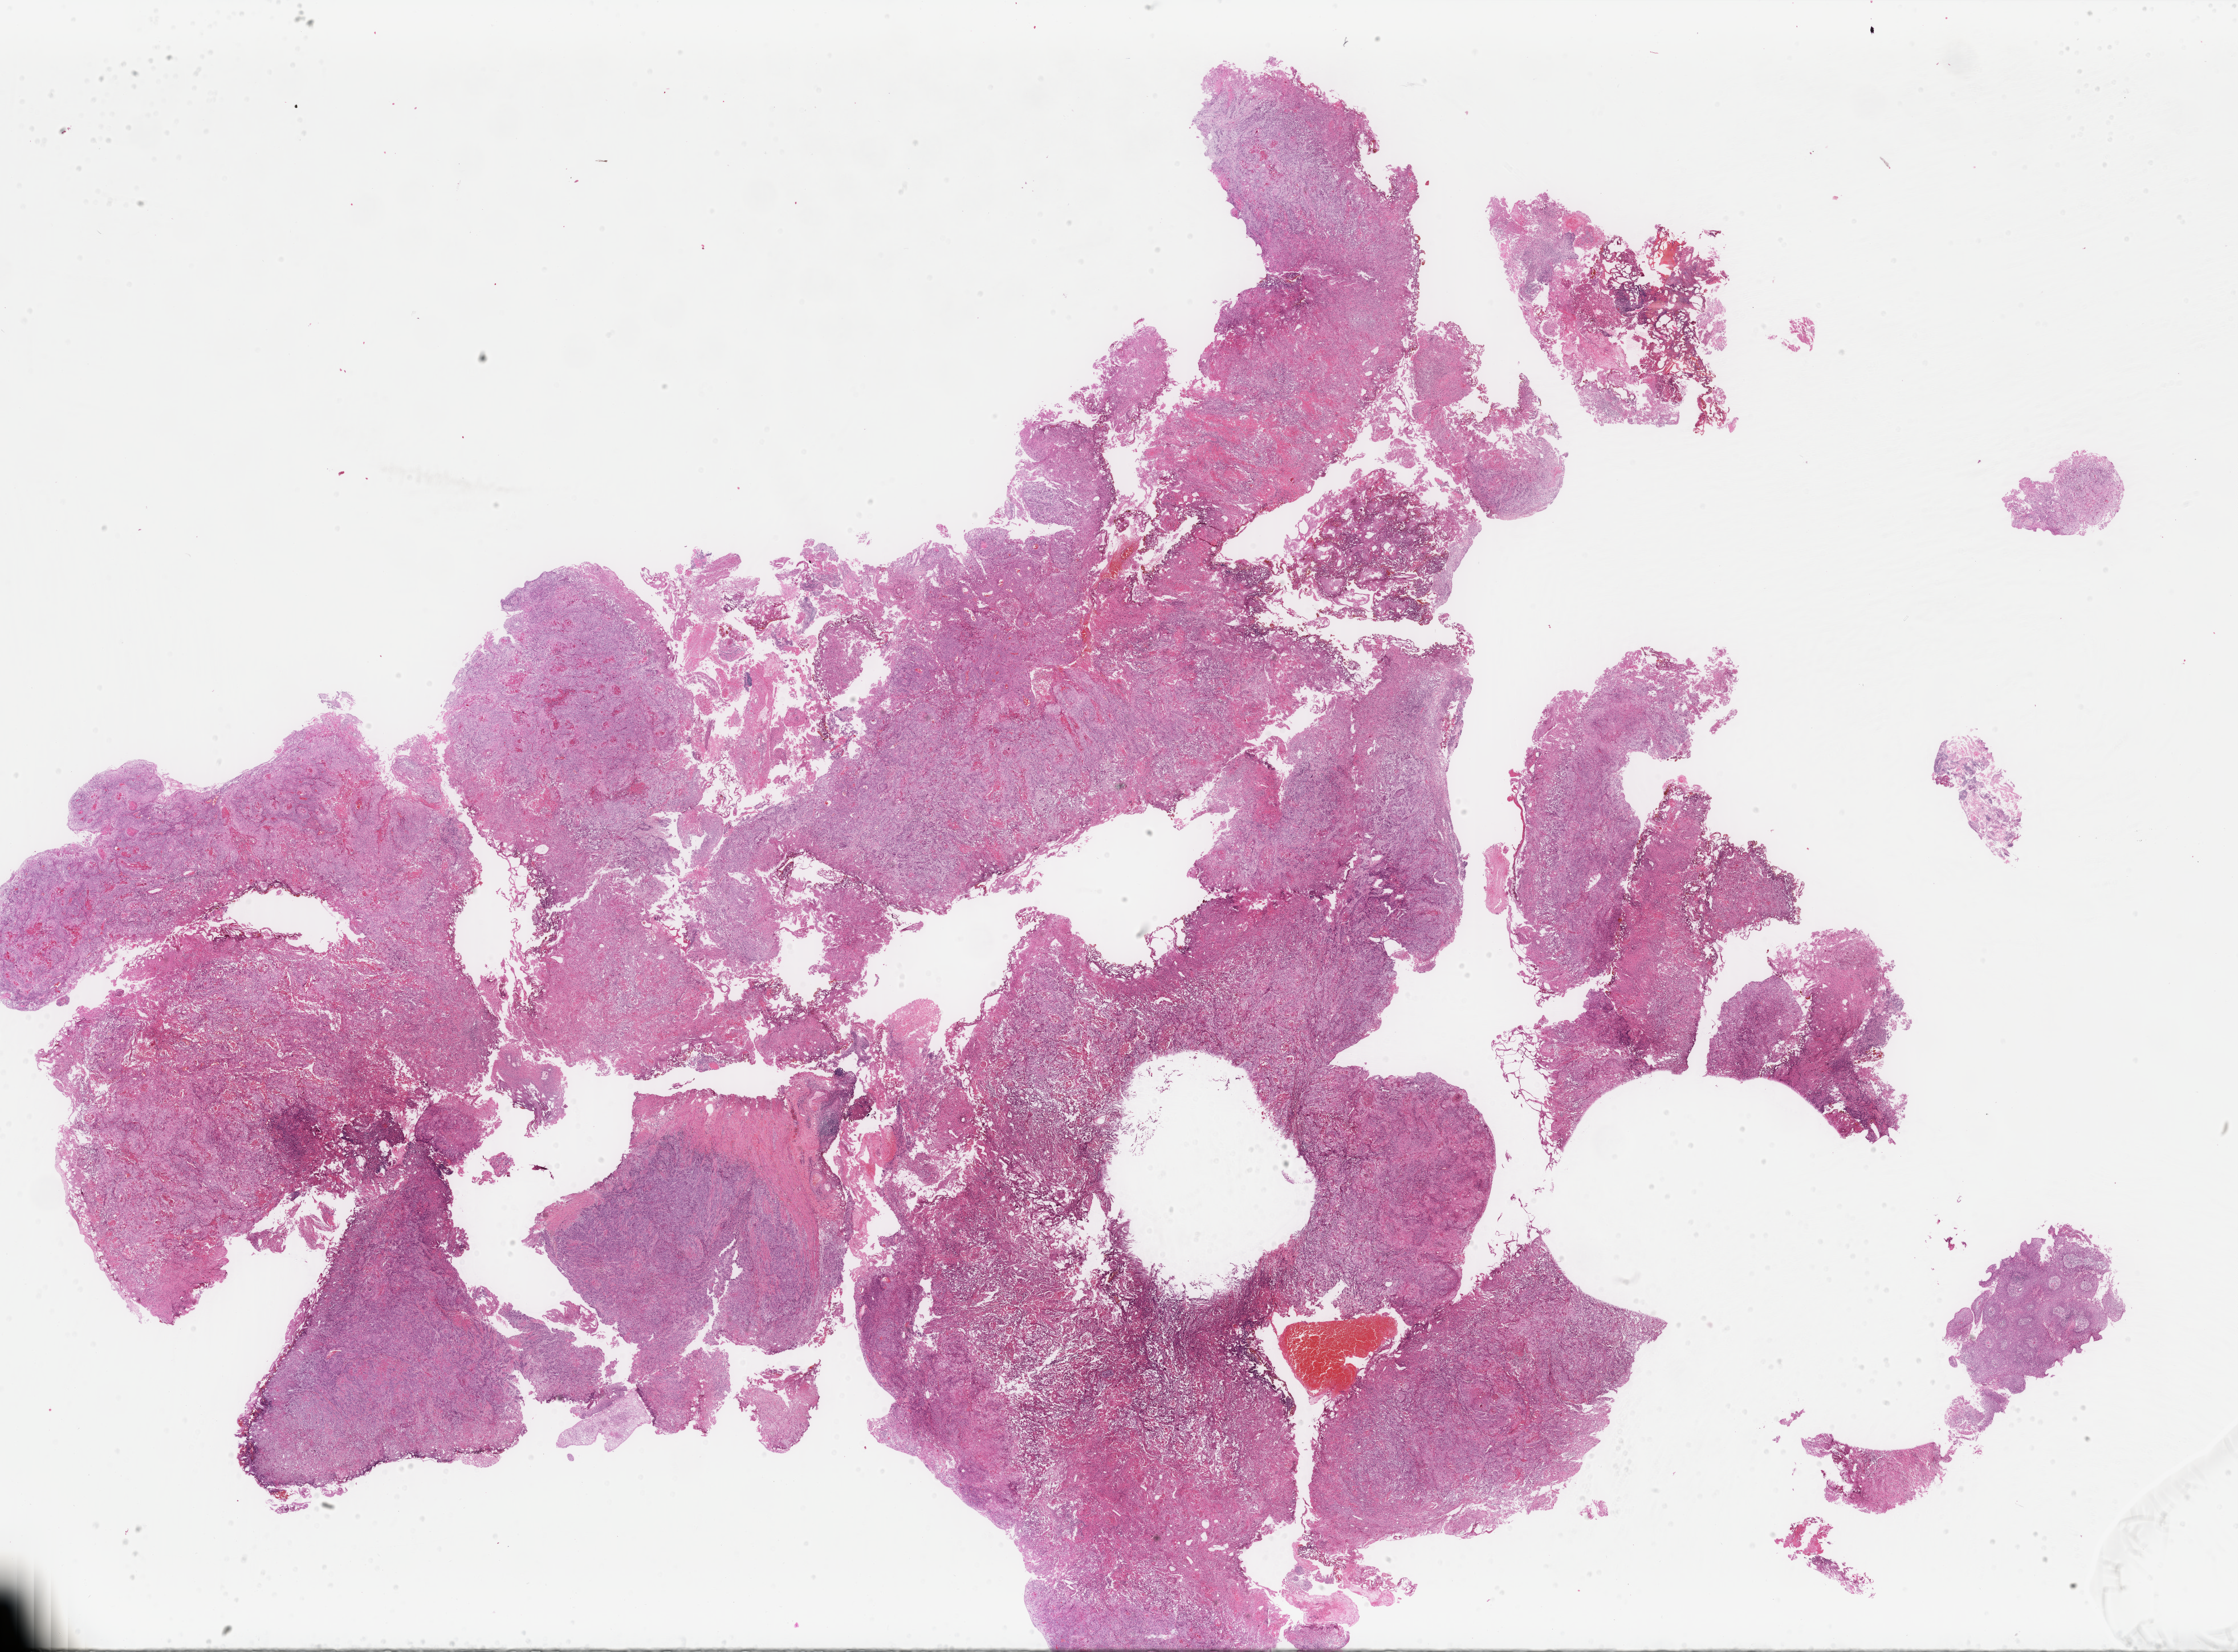
Digitized H&E tissue section (whole slide), shown as a low-resolution overview of the whole scanned area (about 31.2 x 23.0 mm). FFPE section. Sample: primary tumour, bladder. Female, age 56 years at initial diagnosis. Histologic grade: high grade.
TNM: N0 M0. AJCC pathologic stage: II (6th edition). Pathologic diagnosis: Transitional cell carcinoma.